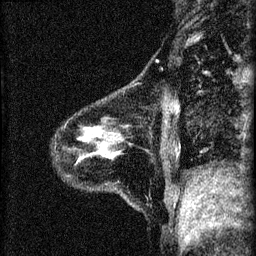
Breast MRI (dynamic contrast-enhanced), one sagittal slice. Position 9 of 60 along the scan axis. Dynamic contrast-enhanced series, image 2 of 4 at this slice position (ordered by acquisition). 1.5 T. TE 4.2 ms, TR 8.2 ms. 2 mm slice thickness. 256 × 256 image matrix, field of view 180 × 180 mm. Female patient, age 41 years.
Structures marked on this image (semi-automatically segmented with operator editing):
- analysis volume of interest (the breast-tissue region the enhancement analysis was run in; not a lesion): bounding box [x1, y1, x2, y2] px = [75, 102, 166, 164]
- tumour enhancement mask (voxels above the 70 % enhancement threshold inside the analysis volume of interest): [113, 154, 115, 156]